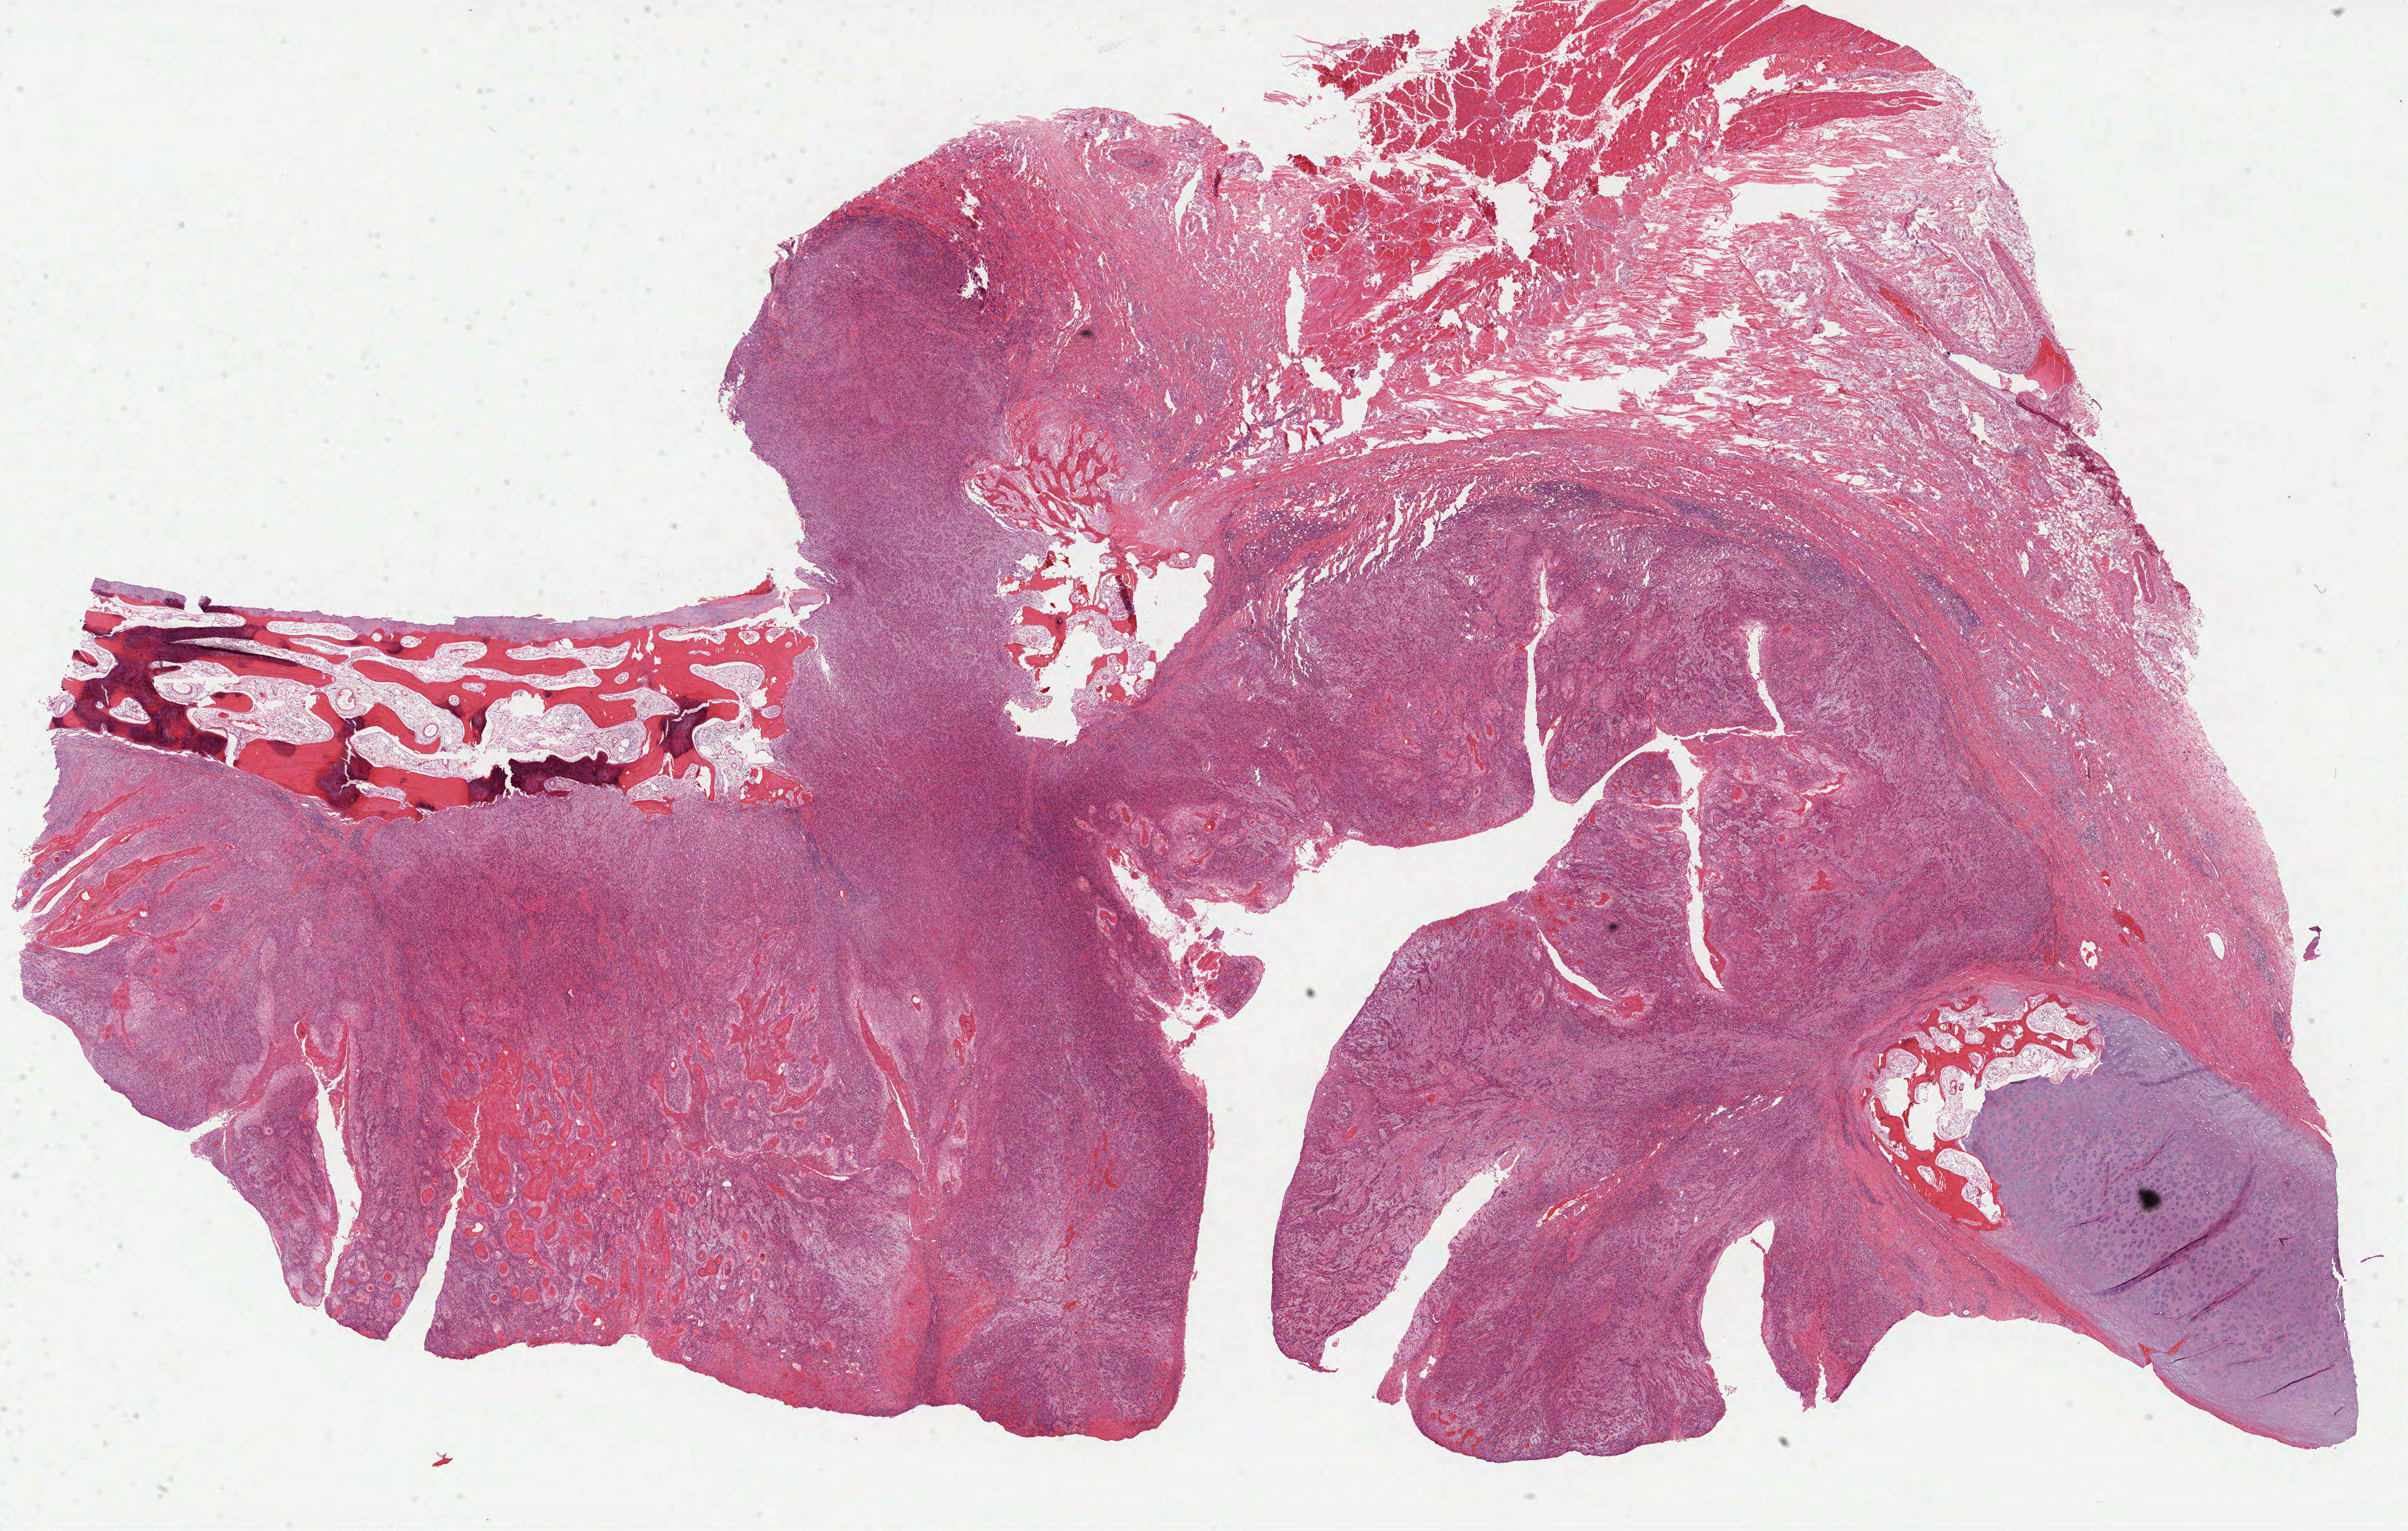
Hematoxylin and eosin (H&E) stained whole-slide image — a low-resolution overview of the entire scanned area, about 27.6 x 17.5 mm (acquisition: 40x scan), formalin-fixed paraffin-embedded (FFPE) diagnostic section, head and neck, primary tumour sample. Male patient; age at initial diagnosis 48 years. Histologic grade: G3 (poorly differentiated).
AJCC pathologic stage: IVB (6th edition). Pathologic diagnosis: Squamous cell carcinoma, NOS (larynx, NOS).